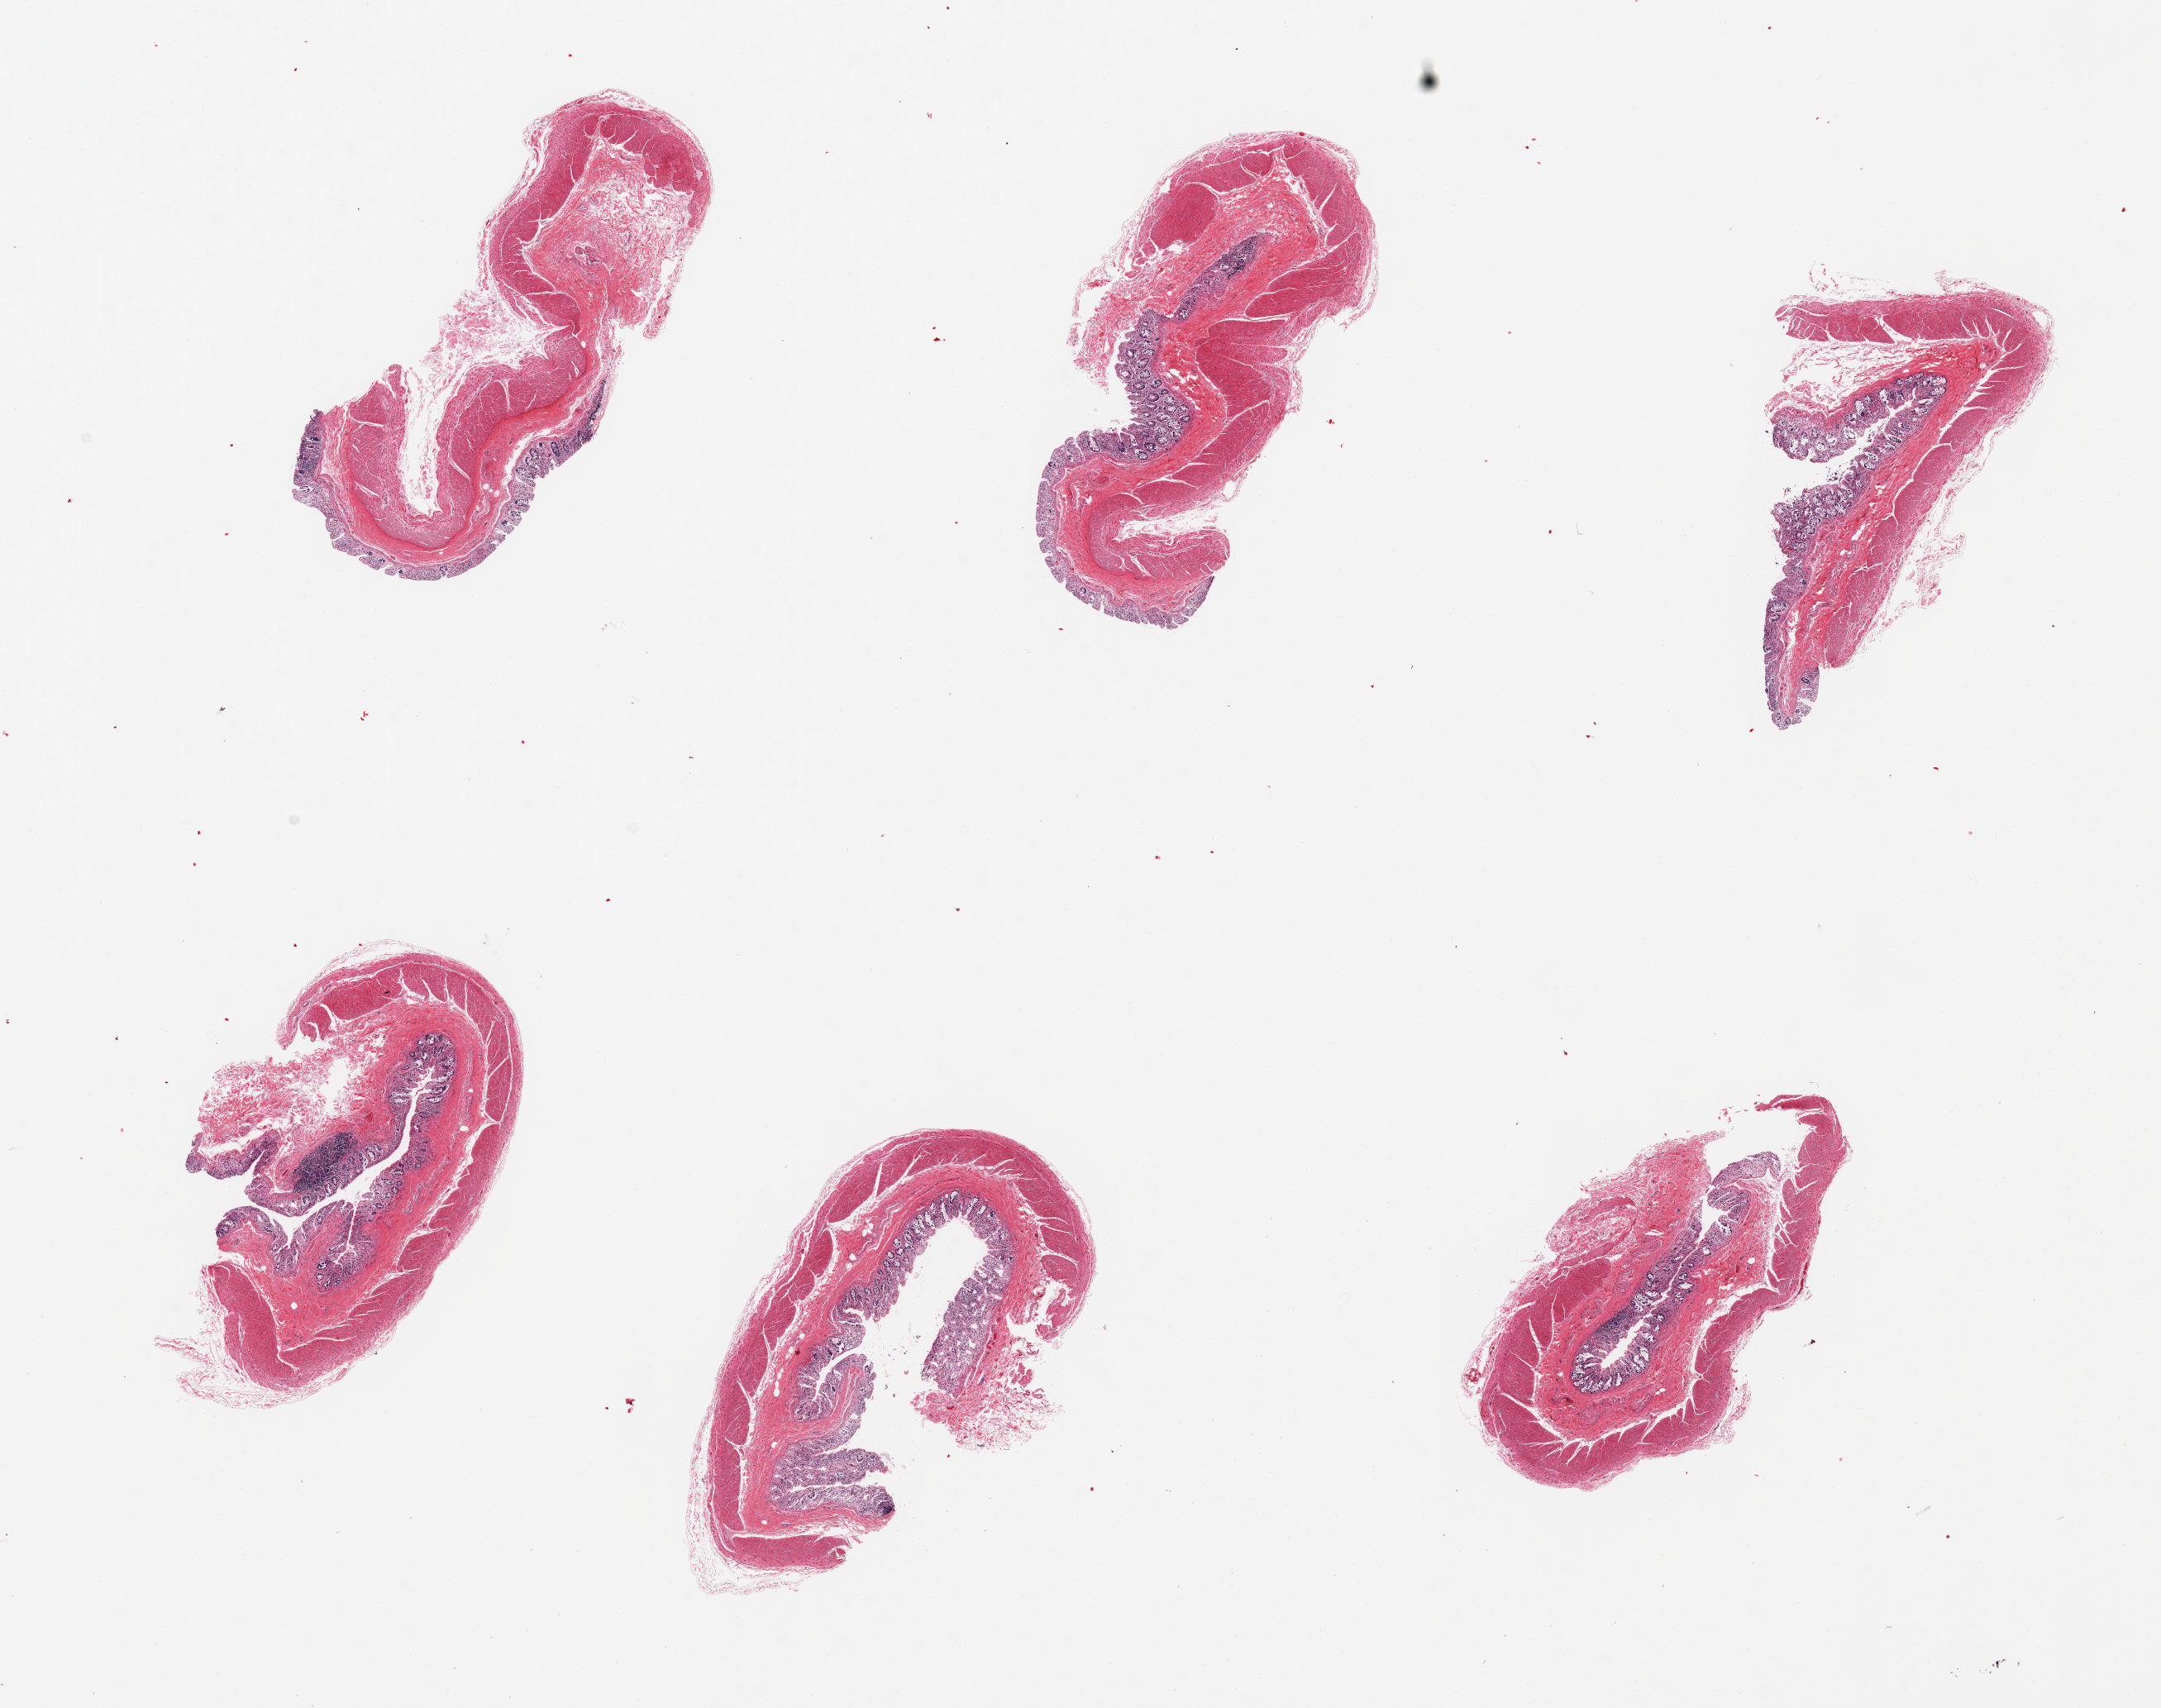
Whole-slide image, haematoxylin and eosin stain, shown as a low-resolution overview of the whole scanned area (about 20.7 x 16.3 mm, acquisition: 20x scan), PAXgene-fixed, paraffin-embedded tissue, target tissue: transverse colon, donor tissue sample. Donor: male.
Review note (as recorded): 6 pieces, mucosa up to ~0.4mm thick, but glandular component totally autolyzed.